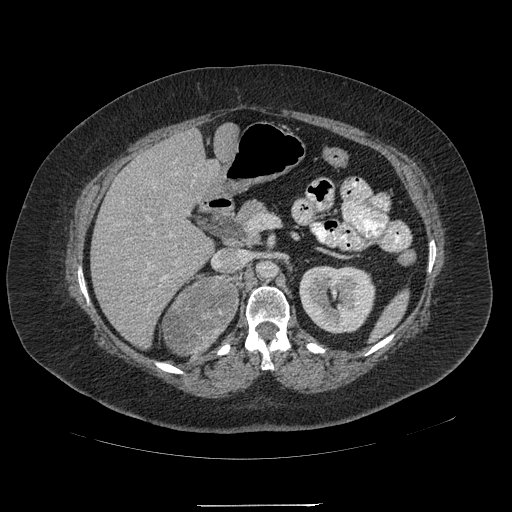
Contrast-enhanced abdominal CT, one axial slice; position 119 of 217 along the scan axis; intravenous contrast given; soft-tissue window (W 400 / L 40 HU); 1.25 mm slice thickness; 512 × 512 image matrix, field of view 453 × 453 mm. Patient: female, 55 years. From the clinical record (not read from this slice): diagnosis: adrenocortical carcinoma; tumour side: right adrenal; tumour size at pathology: 11 cm; Ki-67 index: 20 %; stage (as recorded): 2.
Structures marked on this image (semi-automatic segmentation, software-assisted and operator-edited):
- mass: bounding box (x1, y1, x2, y2) in pixels: (163, 278, 238, 353)